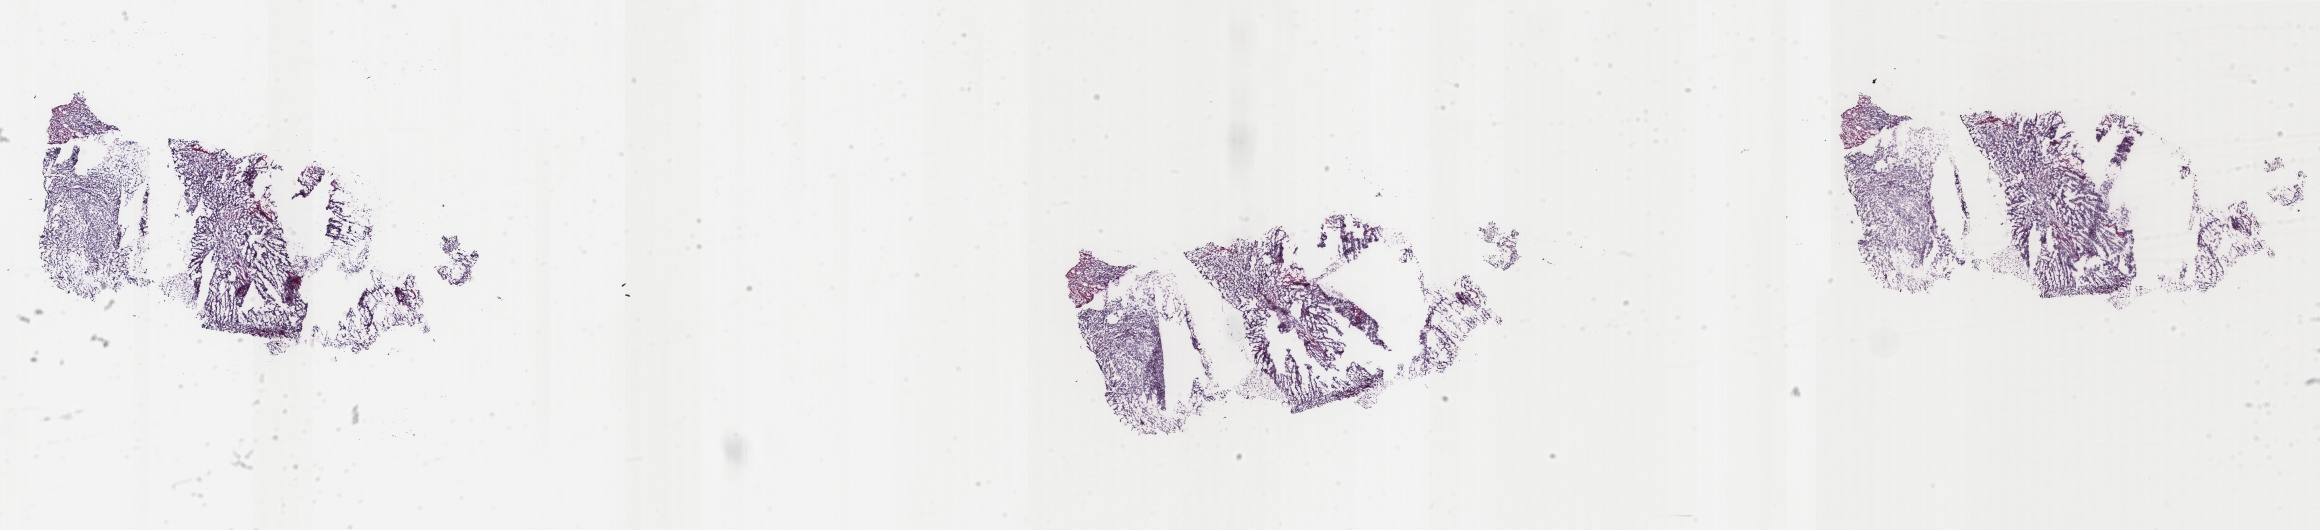
Whole-slide histology image, H&E-stained, shown as a low-resolution overview of the whole scanned area (about 36.8 x 8.4 mm); frozen section from the top of the tissue portion; uterus, primary tumour sample. Female patient; age at initial diagnosis 82 years.
Histologic diagnosis: Endometrioid adenocarcinoma, NOS (endometrium).